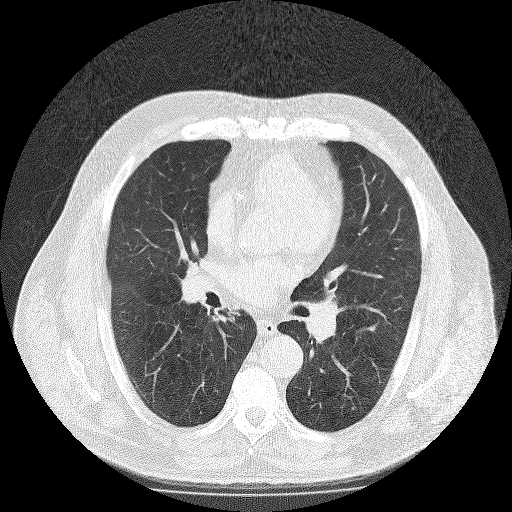
Chest CT (low-dose screening protocol), one axial image; second screening round (one year after baseline); lung window (W 1500 / L -600 HU); 2 mm slice thickness; lung (sharp) reconstruction kernel (FC51). Male, age 65 years at enrolment. Former smoker at enrolment.
• Expert reader's lesion annotation, box from (x=206, y=297) to (x=250, y=331) px.
• The exam's reader record, not a measurement of the box and not confirmed to be the same lesion: non-calcified nodule or mass ≥4 mm, right lower lobe, 10 × 9 mm, spiculated (stellate) margins, soft tissue attenuation, pre-existing on the prior screen: yes; interval growth: no.
• Participant outcome: lung cancer diagnosed 247 days after this screen — large cell neuroendocrine carcinoma, right lower lobe, undifferentiated (G4), stage IIIA (AJCC 6th edition).